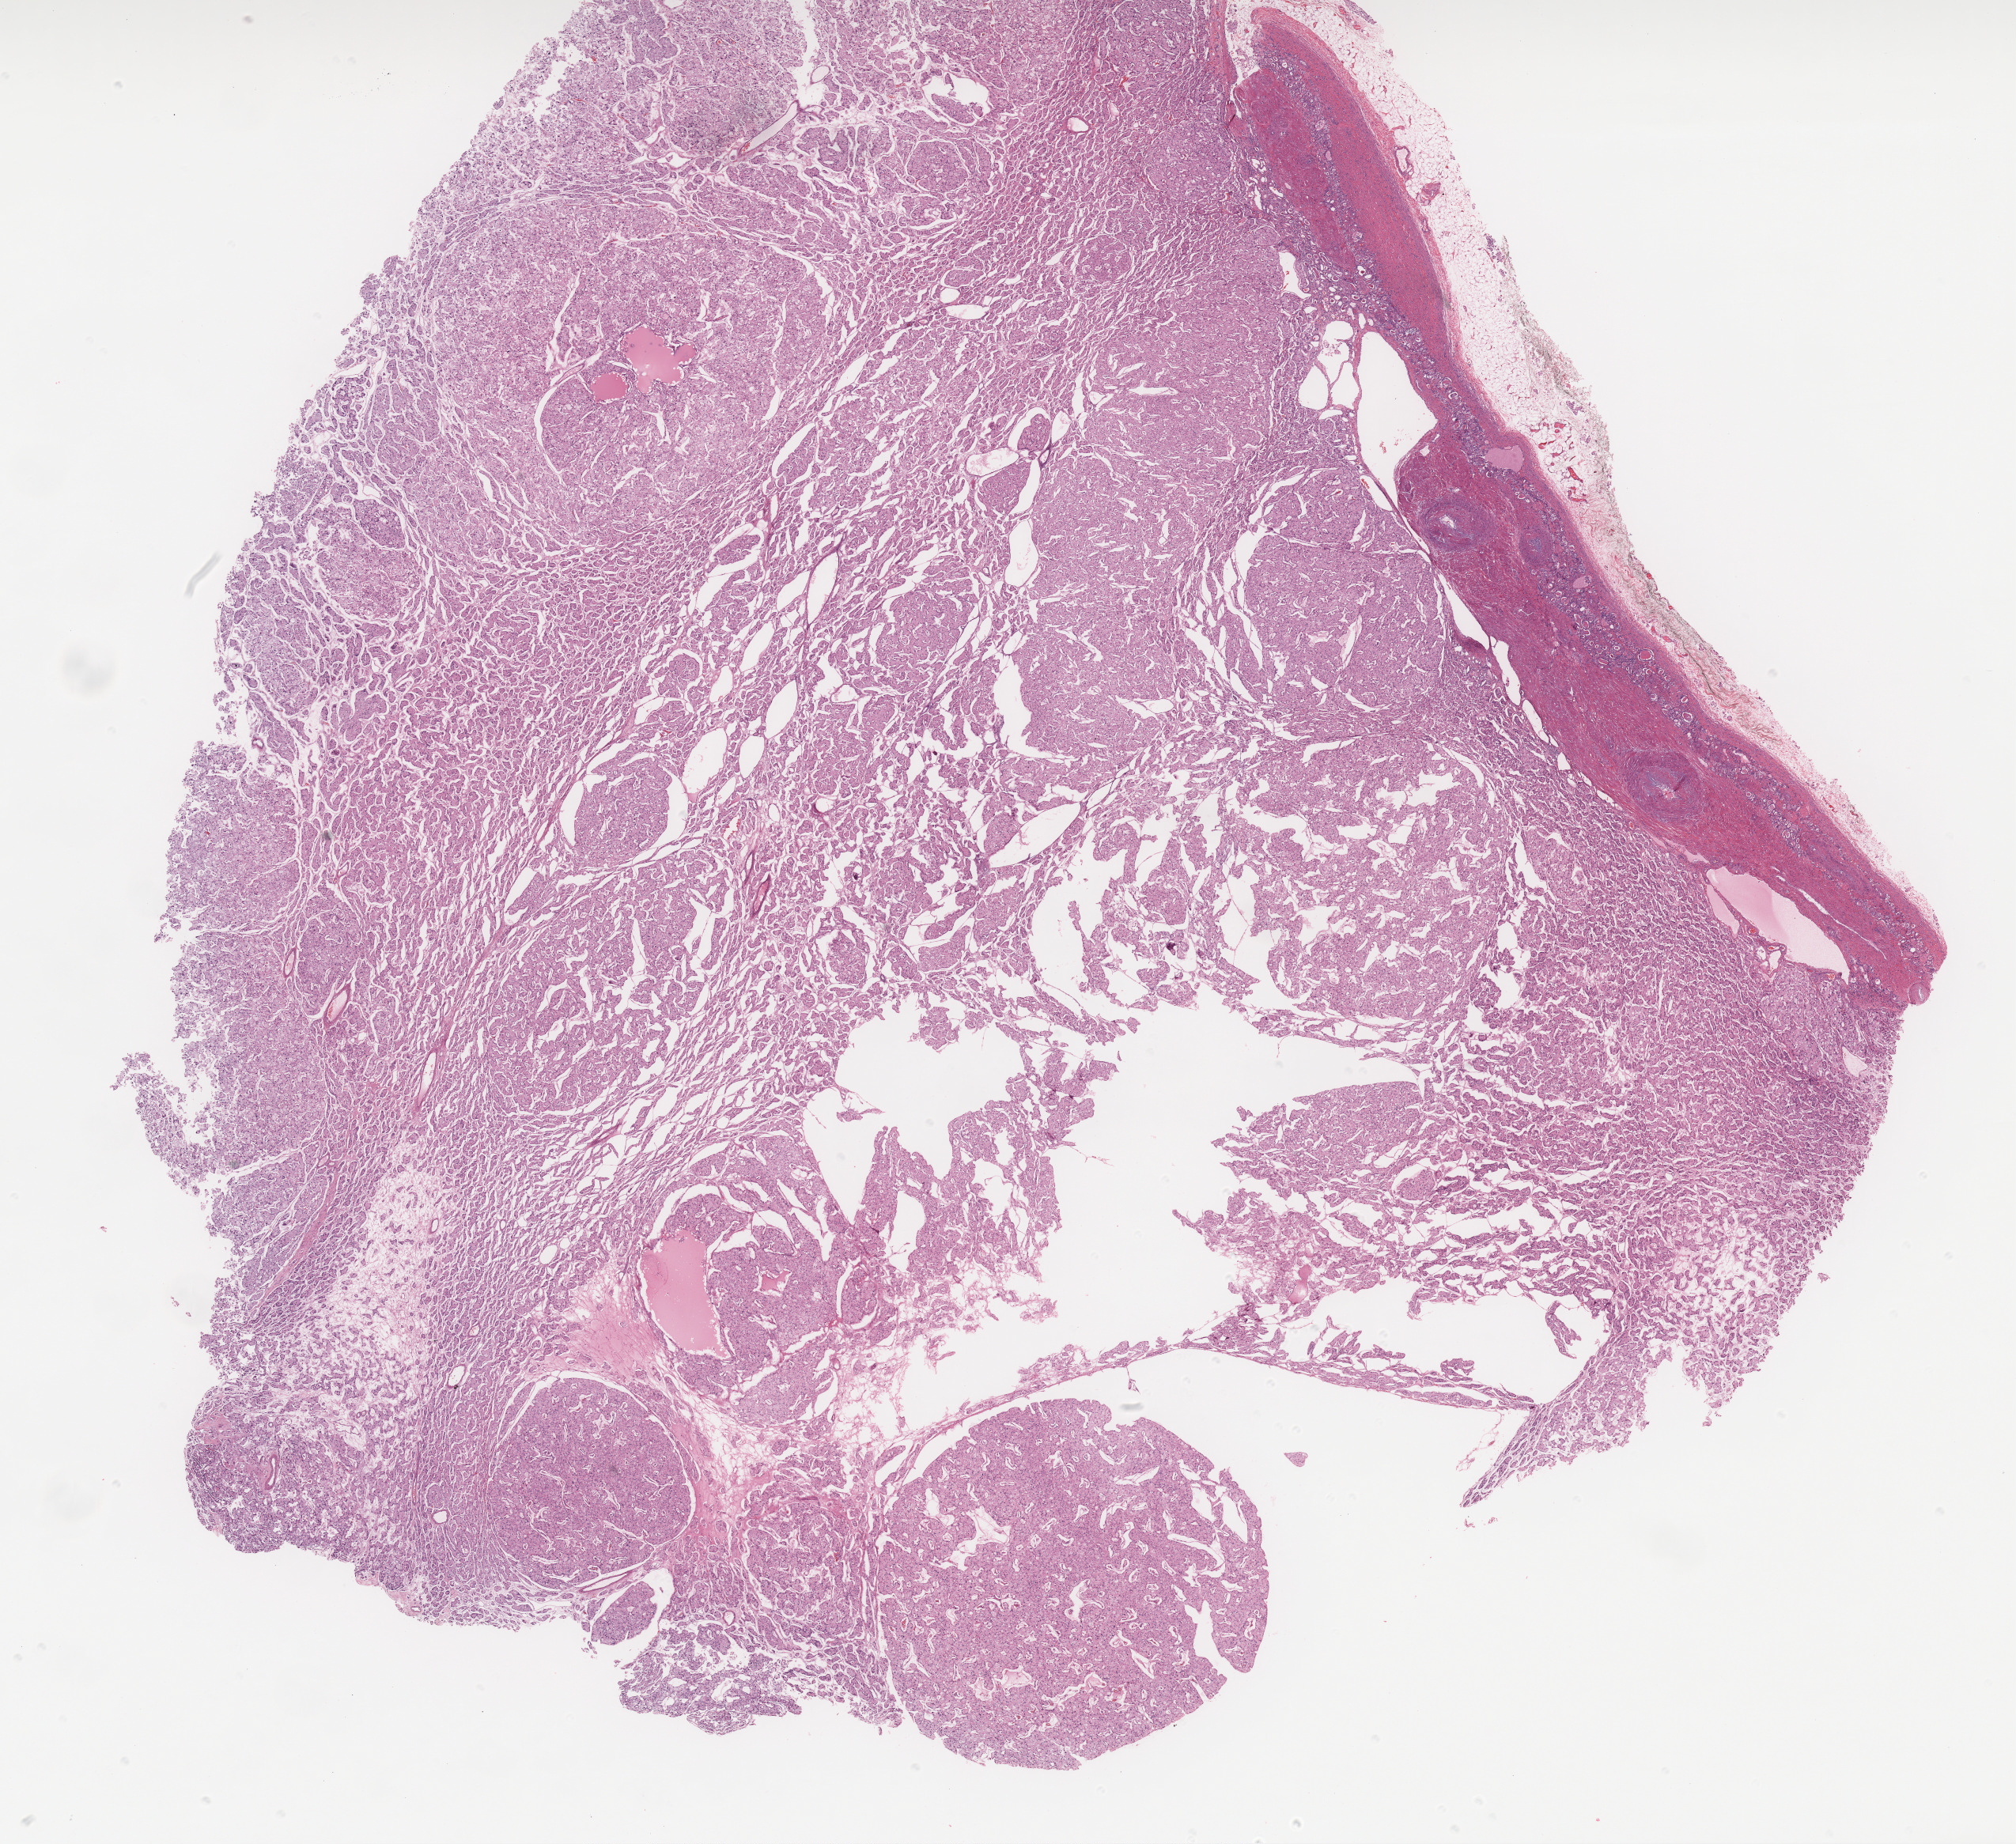
Whole-slide histology image, H&E — low-resolution overview of the scanned area, about 20.4 x 18.6 mm, formalin-fixed paraffin-embedded (FFPE) diagnostic section, kidney, primary tumour sample. Female, age 67 years at initial diagnosis.
Pathologic diagnosis: Renal cell carcinoma, chromophobe type. AJCC pathologic stage: II (5th edition).